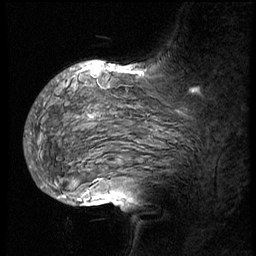
Breast MRI (dynamic contrast-enhanced), one sagittal slice; slice 38 of 56 in the series (ordered by position); 3 images stored at this slice position (order not interpretable as contrast timing); 1.5 T; TE 4.2 ms, TR 8.9 ms; 3 mm slice thickness; 256 × 256 image matrix, field of view 220 × 220 mm. Female patient, age 57 years. Case-level facts recorded for this patient, not image findings: setting: breast cancer imaged before/during neoadjuvant chemotherapy; receptor status: HER2-positive.
Outlined on this slice (semi-automatic segmentation, software-assisted and operator-edited):
- analysis volume of interest (the breast-tissue region the enhancement analysis was run in; not a lesion): box from (x=28, y=70) to (x=228, y=156) px
- tumour enhancement mask (voxels above the 140 % enhancement threshold inside the analysis volume of interest): (x=82, y=70)–(x=199, y=118)